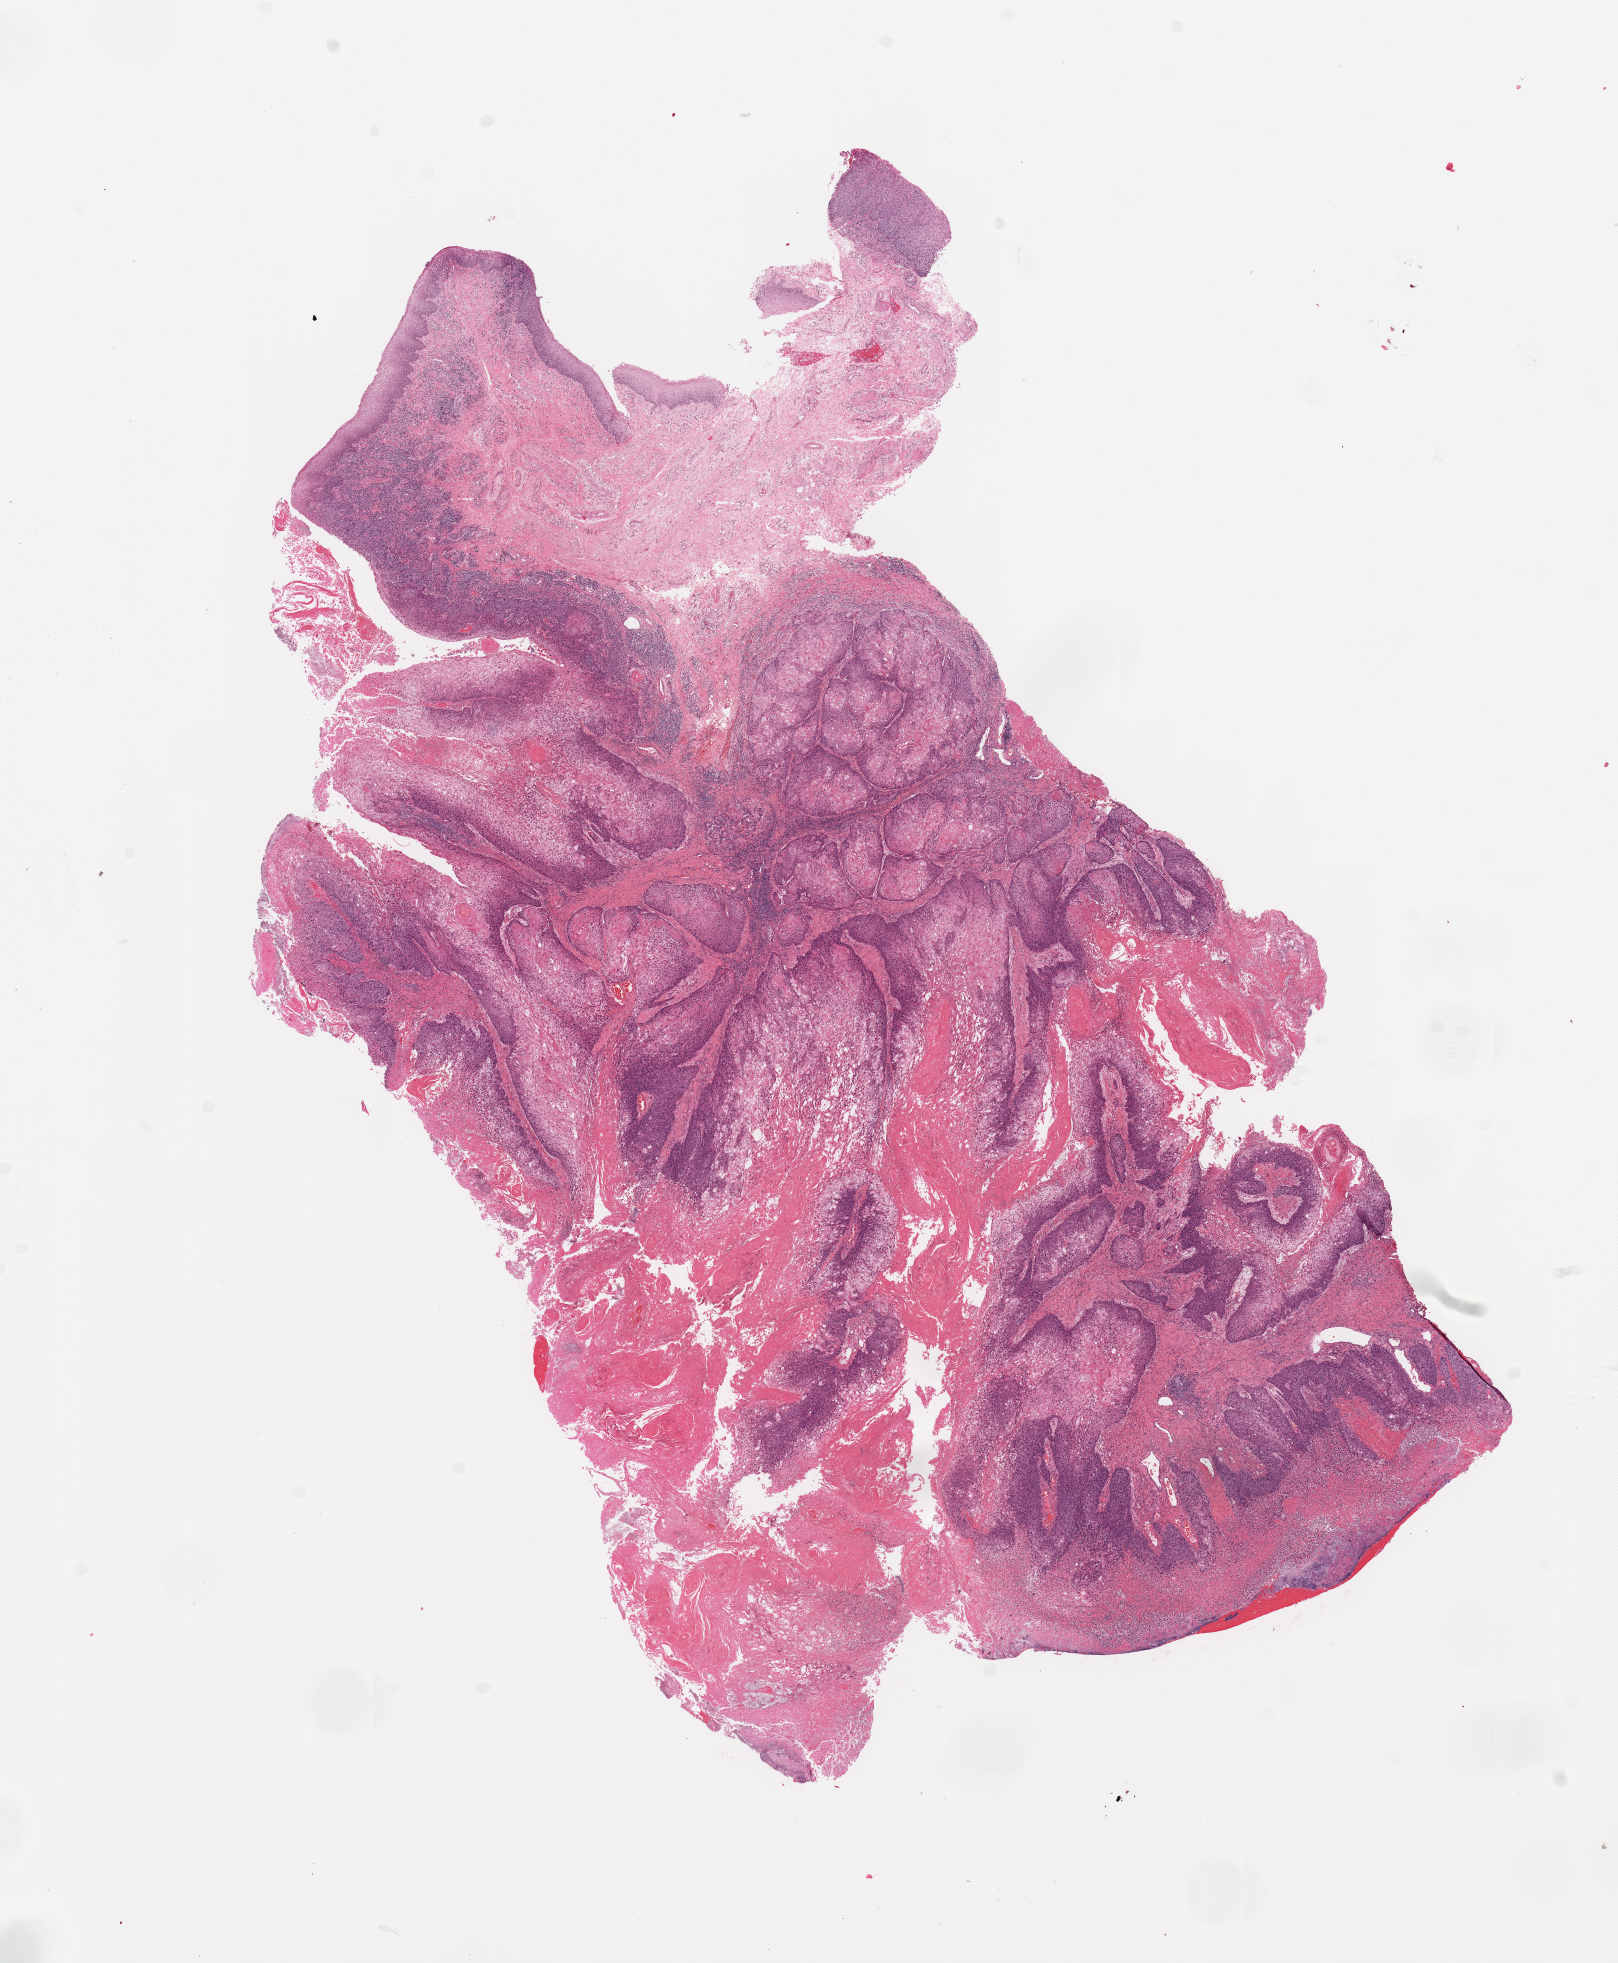
H&E-stained whole-slide image, low-resolution overview of the scanned area, about 12.8 x 15.5 mm (from a 20x scan), tumour tissue sample, sampled site: larynx. Patient: male, age 62 years. Slide review estimates, as recorded: tumour nuclei 80%, necrosis 20%.
Diagnosis: Squamous cell carcinoma, NOS.